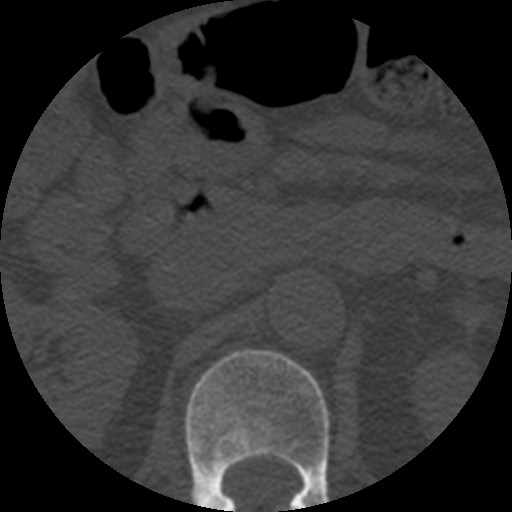
CT including the spine, one axial slice. Slice 190 of 508 in the series (ordered by position). Reconstruction kernel STANDARD. 120 kVp. Bone window (W 1800 / L 400 HU). 1.25 mm slice thickness. 512 × 512 image matrix, field of view 160 × 160 mm. Patient age 57 years. Case-level facts recorded for this patient, not image findings: primary cancer: prostate.
Annotated regions visible in this slice (semi-automatic segmentation, software-assisted and operator-edited):
- L1 vertebra: bounding box [x1, y1, x2, y2] px = [185, 349, 330, 512]